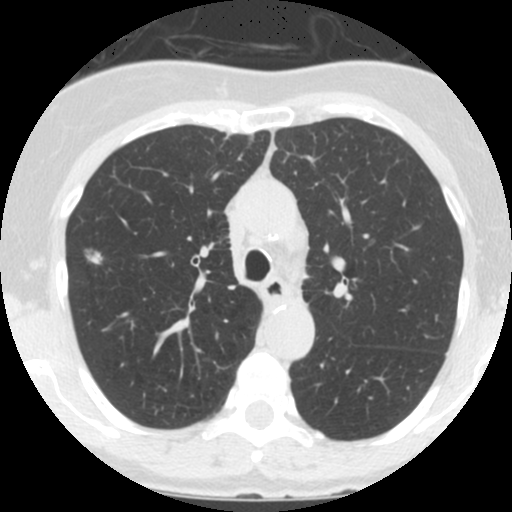
Low-dose screening chest CT, one axial slice. Slice 101 of 146 in the series (ordered by position). Lung window (W 1500 / L -600 HU). 512 × 512 image matrix.
Outlined on this slice (manually delineated by an expert):
- lesion 1 (tumor, upper lobe of right lung): bounding box [x1, y1, x2, y2] px = [83, 248, 105, 265]